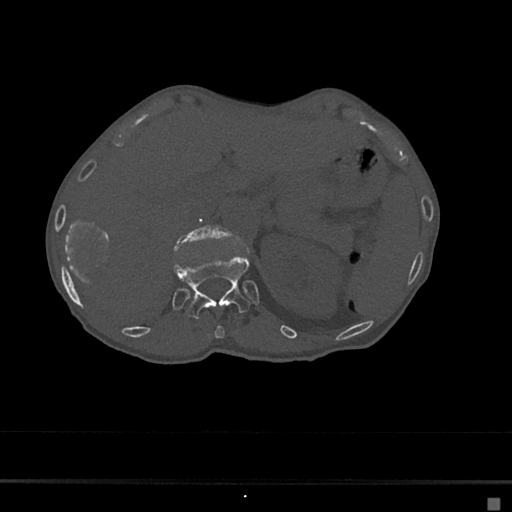
CT including the spine, one axial slice. Slice 123 of 797 in the series (ordered by position). 120 kVp. Bone window (W 1800 / L 400 HU). 0.5 mm slice thickness. 512 × 512 image matrix, field of view 360 × 360 mm. Patient: female, 68 years. From the clinical record (not read from this slice): primary cancer: renal.
Annotated regions visible in this slice (semi-automatic segmentation, software-assisted and operator-edited):
- L1 vertebra: box from (x=177, y=225) to (x=229, y=246) px
- T11 vertebra: (x=214, y=325)–(x=225, y=339)
- T12 vertebra: (x=173, y=254)–(x=250, y=320)